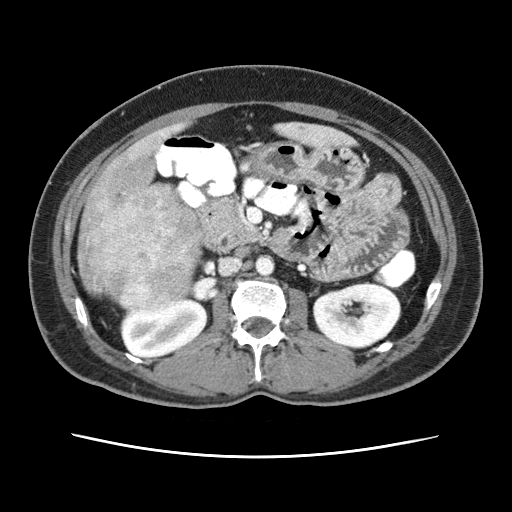
Contrast-enhanced abdominal CT (liver protocol), one axial slice; slice 13 of 79 in the series (ordered by position); reconstruction kernel STANDARD; soft-tissue window (W 400 / L 40 HU); 2.5 mm slice thickness; 512 × 512 image matrix, field of view 340 × 340 mm. From the clinical record (not read from this slice): diagnosis: hepatocellular carcinoma (patient treated with transarterial chemoembolisation; whether this scan precedes or follows treatment is not stated here); TNM stage (as recorded): Stage-I; Child-Pugh class: A.
Structures marked on this image (semi-automatically segmented with operator editing):
- abdominal aorta: box from (x=255, y=255) to (x=274, y=275) px
- liver parenchyma outside the tumour (the mass and vessels are separate outlines, so this box may not span the whole liver): (x=78, y=130)–(x=242, y=298)
- mass: (x=78, y=169)–(x=204, y=311)